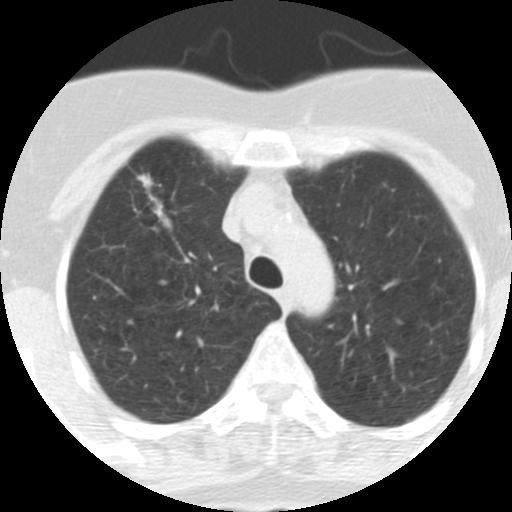
Low-dose screening chest CT, one axial slice; slice 246 of 313 in the series (ordered by position); reconstruction kernel STANDARD; 120 kVp; lung window (W 1500 / L -600 HU); 512 × 512 image matrix, field of view 253 × 253 mm.
Annotated regions visible in this slice (manually delineated by an expert):
- lesion 1 (tumor, upper lobe of right lung): bounding box <138,174,171,228> (left, top, right, bottom; pixels)